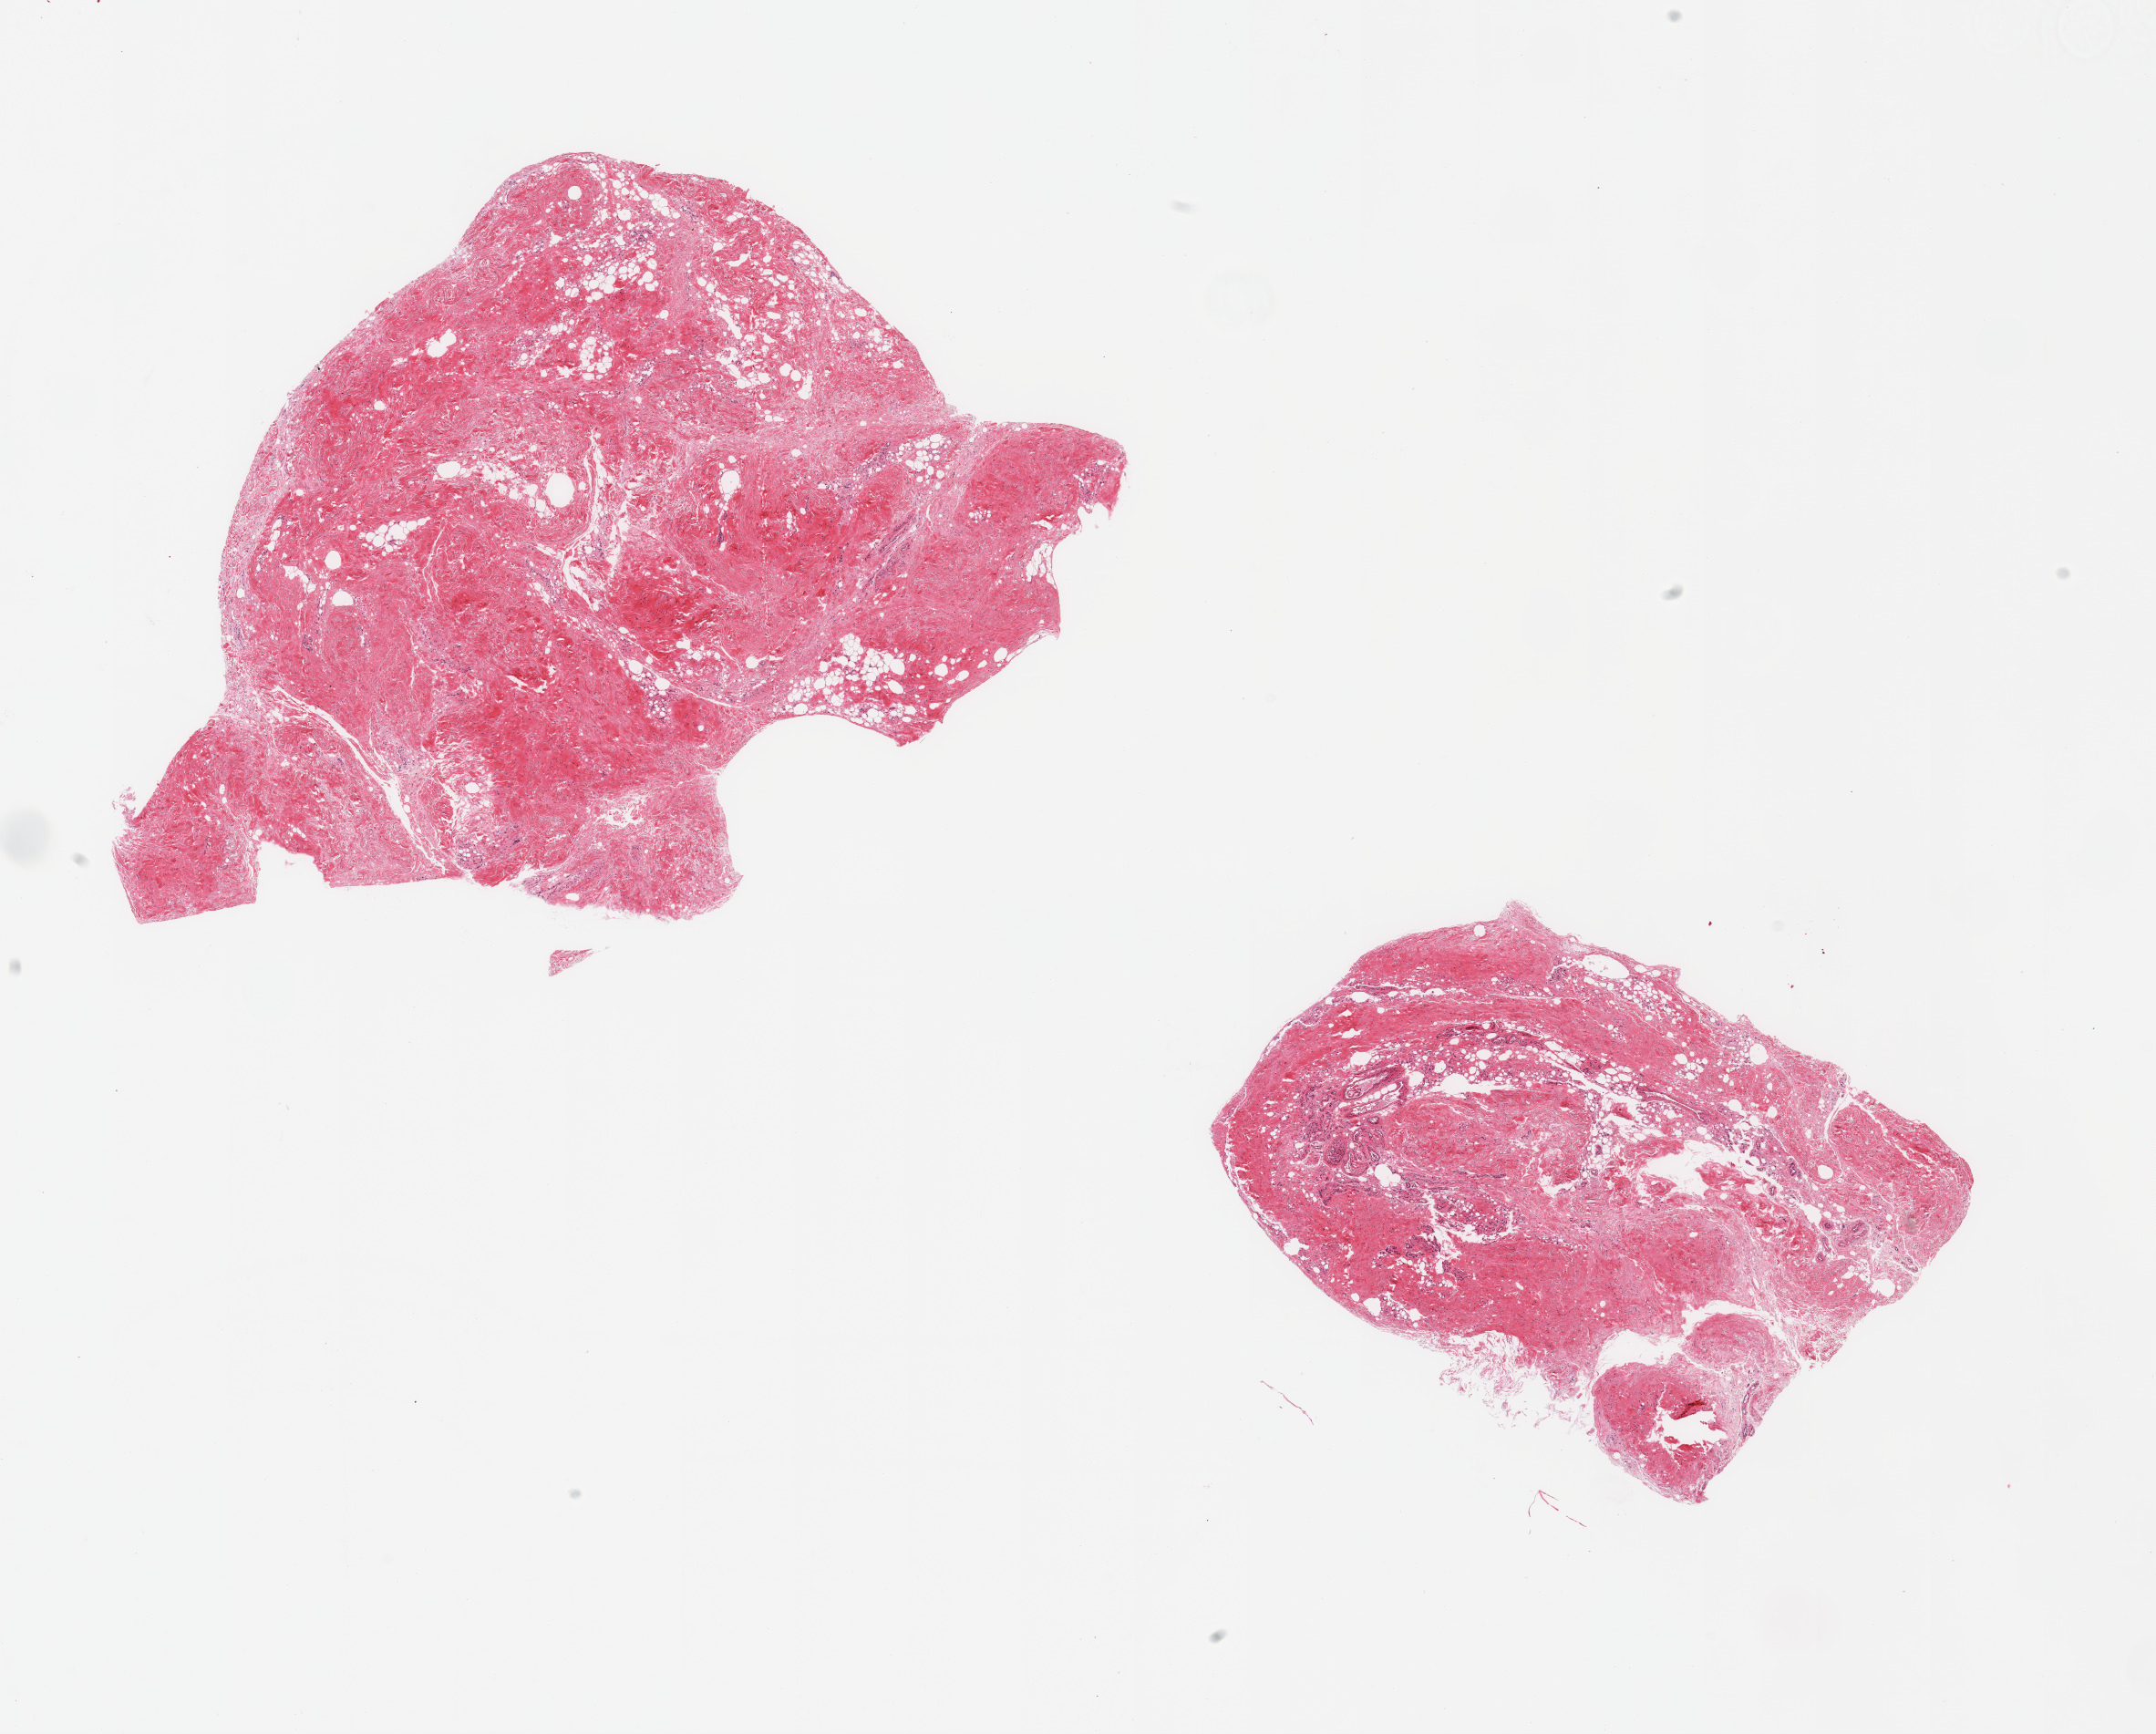
Whole-slide image, hematoxylin and eosin (H&E) stain — low-resolution overview of the scanned area, about 18.7 x 15.0 mm (slide scanned at 20x), PAXgene-fixed paraffin-embedded (PFPE) section, sampled site (target tissue): breast, donor tissue sample.
Pathologist's review note for this sample: 2 pieces; predominantly fibrovascular tissue with minimal adipose tissue; no ductal structures present.